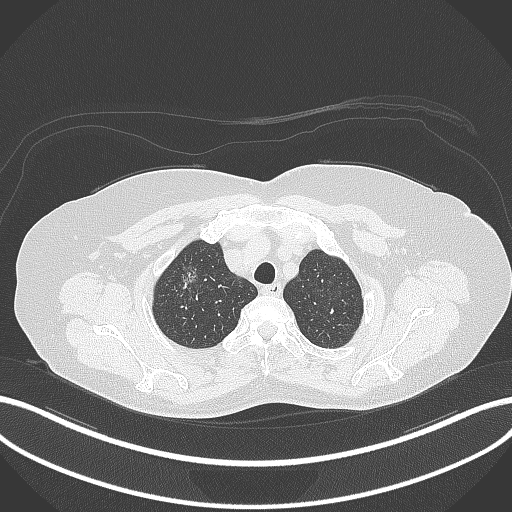
Chest CT, one axial slice. Slice 299 of 365 in the series (ordered by position). Reconstruction kernel B70f. 120 kVp. Lung window (W 1500 / L -600 HU). 1 mm slice thickness. 512 × 512 image matrix, field of view 400 × 400 mm. Female patient, age 62 years. From the clinical record (not read from this slice): clinical TNM (as recorded): T1c N0 M0.
Structures marked on this image (rectangle marked by the reading radiologist):
- lung tumour (recorded histology: adenocarcinoma): bounding box <171,249,208,292> (left, top, right, bottom; pixels)